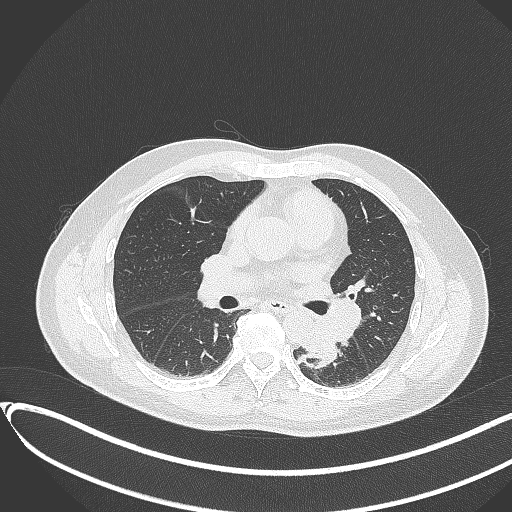
Chest CT, one axial slice. Slice 186 of 417 in the series (ordered by position). Reconstruction kernel B70f. 120 kVp. Lung window (W 1500 / L -600 HU). 1 mm slice thickness. 512 × 512 image matrix, field of view 400 × 400 mm. Patient: male, 54 years. From the clinical record (not read from this slice): clinical TNM (as recorded): T3 N0 M0.
Annotated regions visible in this slice (bounding box drawn by a radiologist):
- lung tumour (recorded histology: squamous cell carcinoma): bounding box [x1, y1, x2, y2] px = [298, 314, 342, 371]